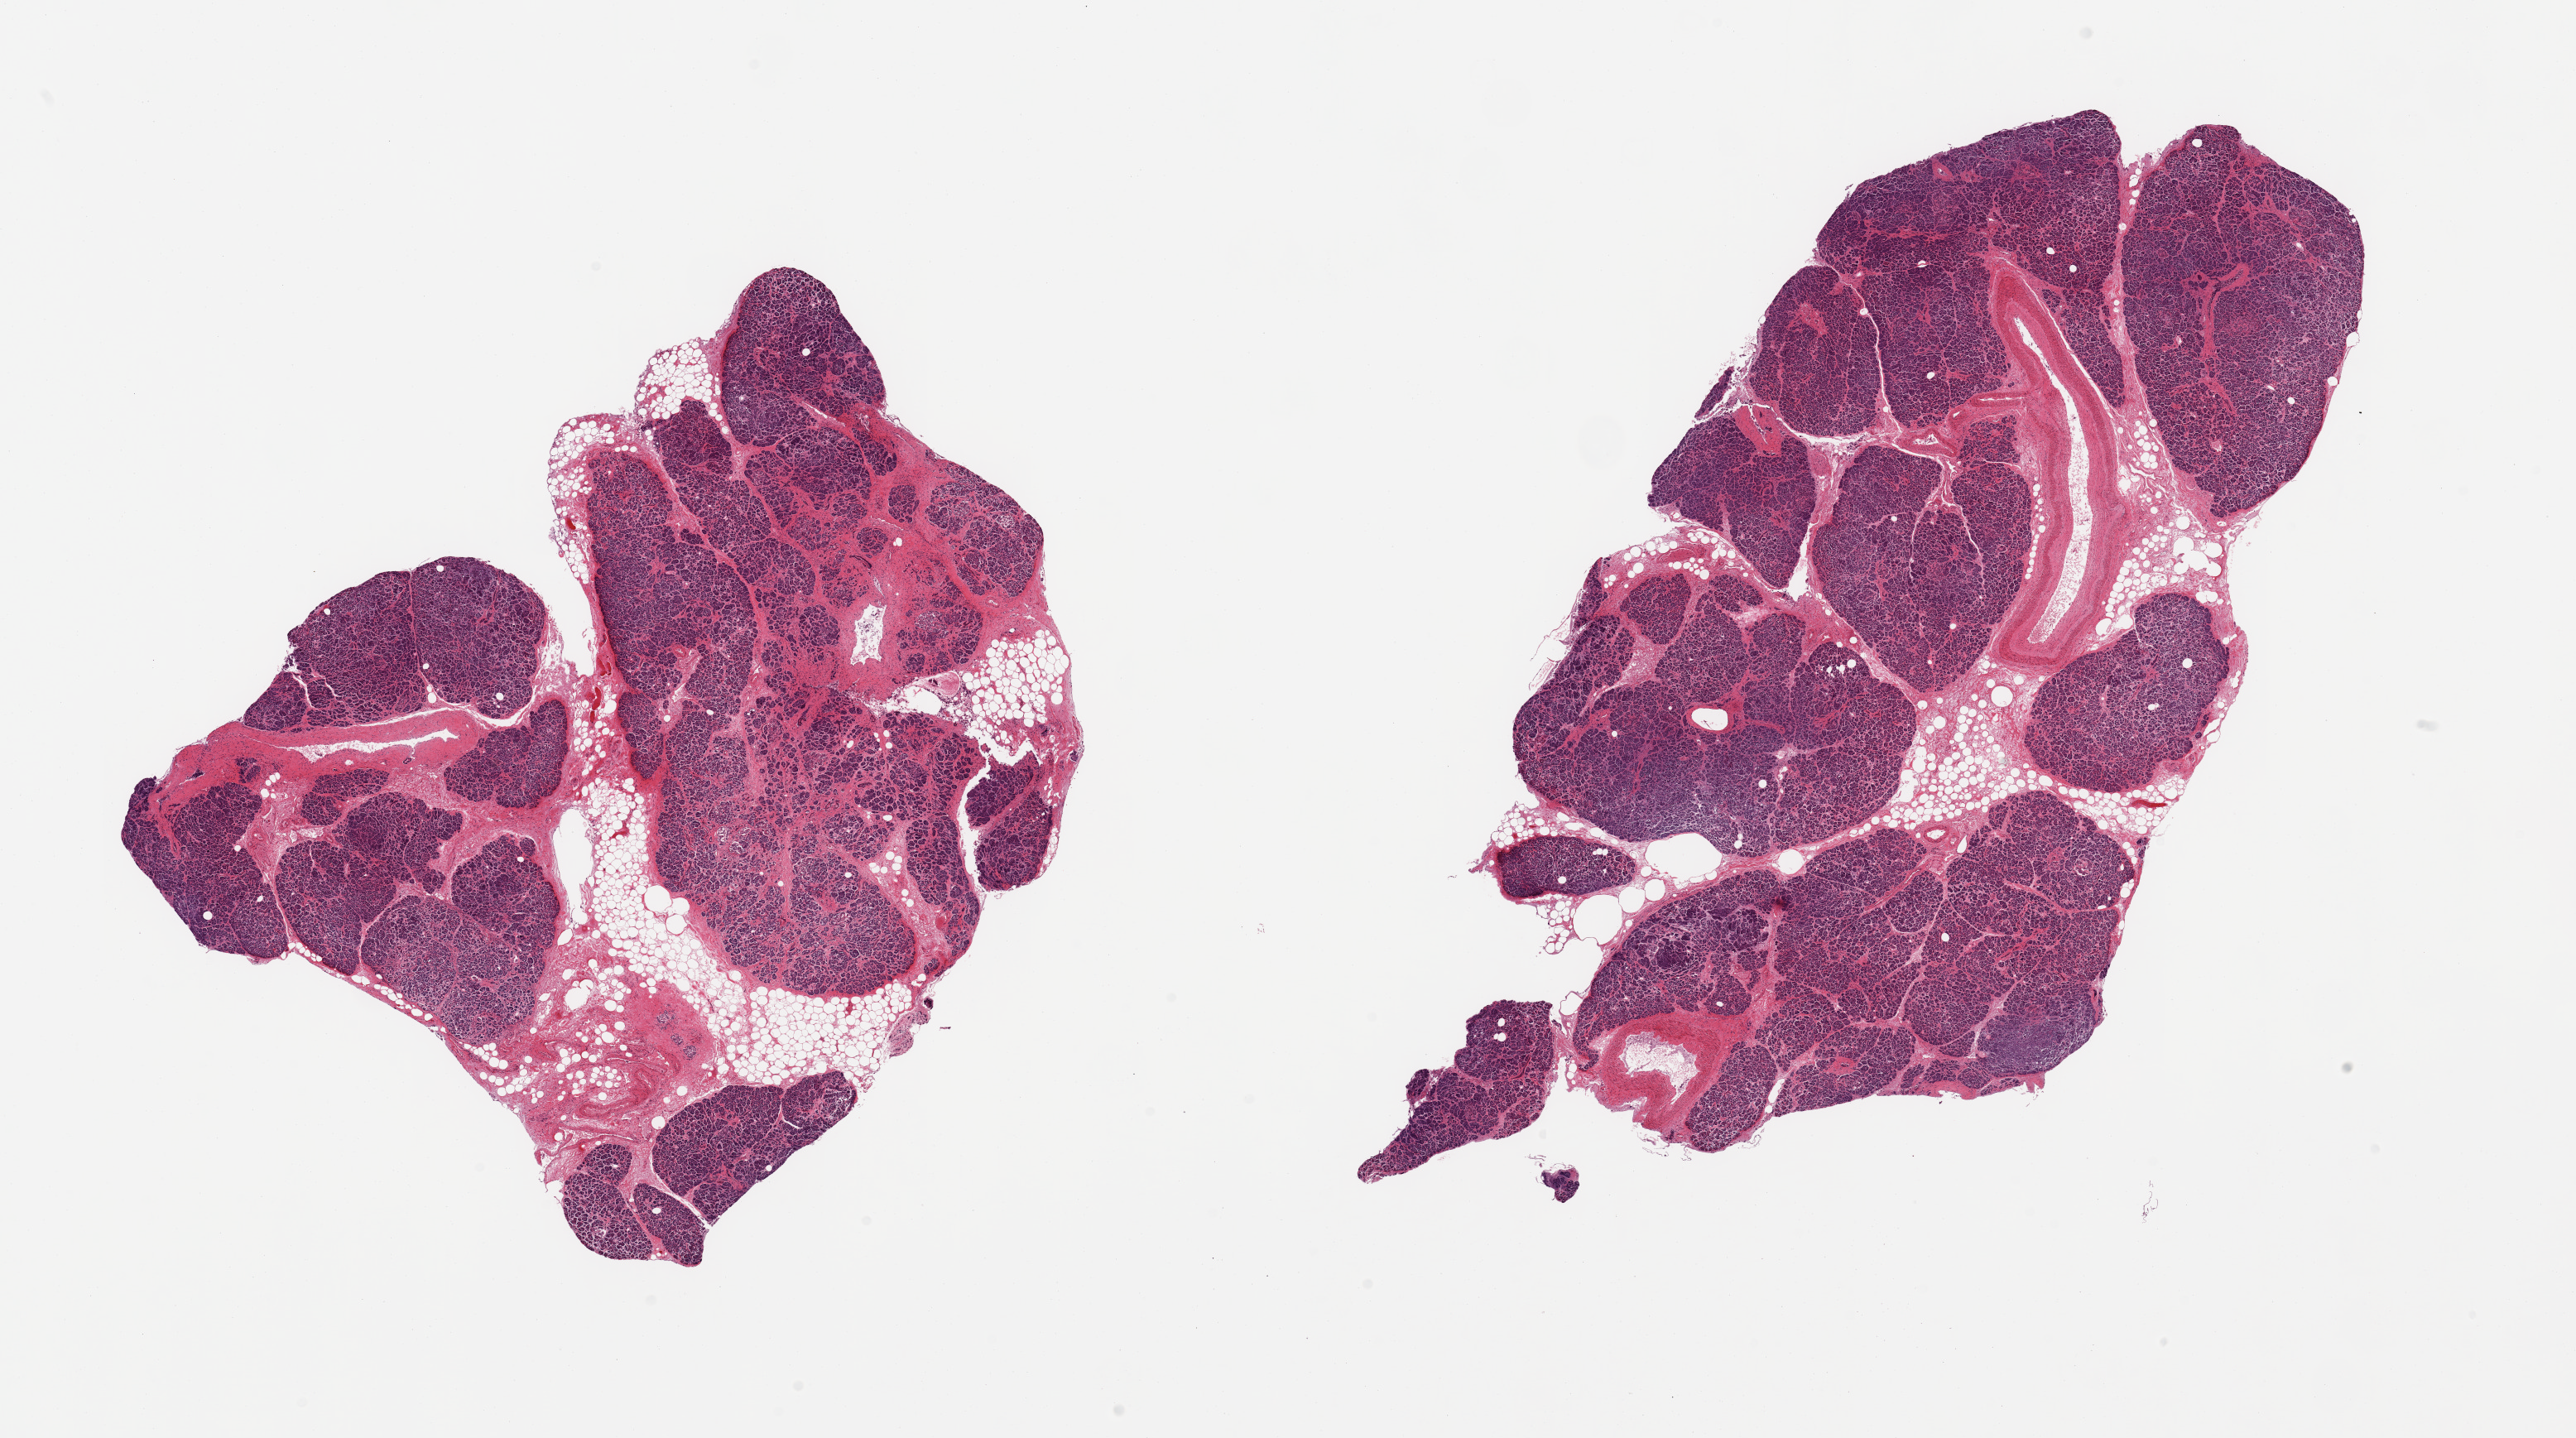
Digitized H&E-stained section — shown as a low-resolution overview of the whole scanned area (about 24.6 x 13.7 mm, acquisition: 20x scan), PAXgene-fixed paraffin-embedded (PFPE) section, section of pancreas (target tissue), donor tissue sample. Female donor.
Pathologist's review note for this sample: 2 pieces; 20% internal adipose and artery; 10% interstitial fibrosis and glandular atrophy.